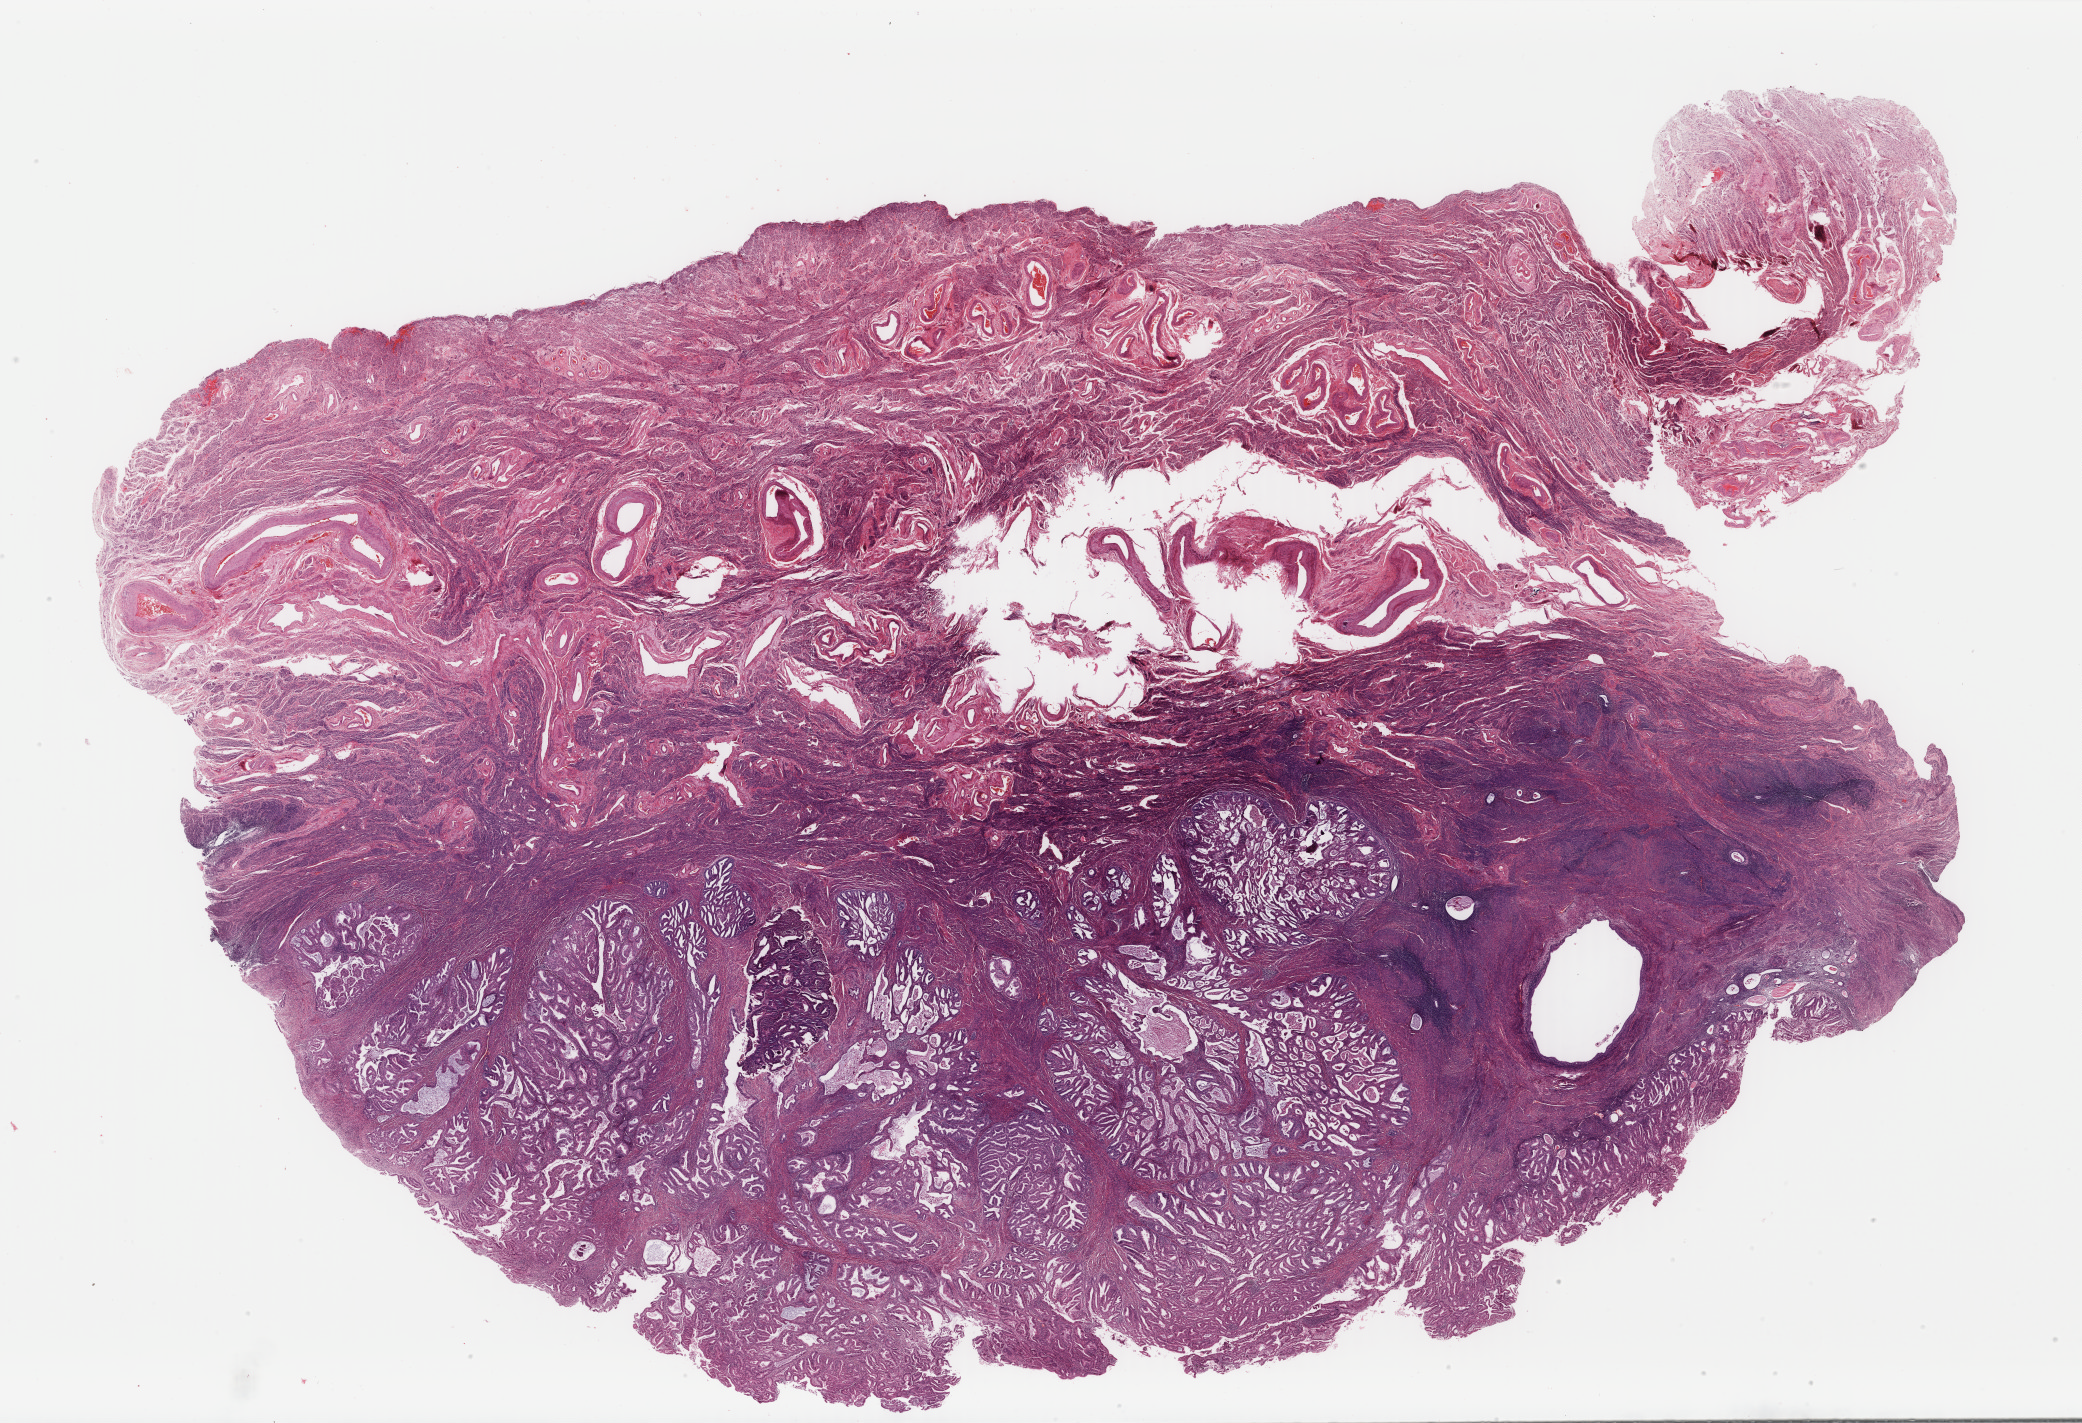
Hematoxylin and eosin (H&E) stained whole-slide image, whole scanned area (about 33.1 x 22.6 mm, slide scanned at 40x) shown as a low-resolution overview; FFPE section; uterus, primary tumour sample. Patient: female, age at initial diagnosis 76 years.
Histologic diagnosis: Endometrioid adenocarcinoma, NOS (endometrium).